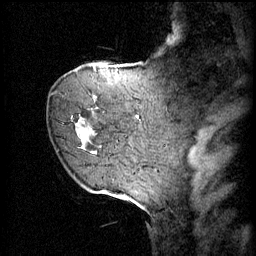
Breast MRI (dynamic contrast-enhanced), one sagittal slice. Position 13 of 60 along the scan axis. 4 images stored at this slice position (order not interpretable as contrast timing). 1.5 T. TE 4.2 ms, TR 11 ms. 2 mm slice thickness. 256 × 256 image matrix. Female patient, age 72 years.
Annotated regions visible in this slice (semi-automatically segmented with operator editing):
- analysis volume of interest (the breast-tissue region the enhancement analysis was run in; not a lesion): bounding box [x1, y1, x2, y2] px = [63, 68, 109, 153]
- tumour enhancement mask (voxels above the 70 % enhancement threshold inside the analysis volume of interest): [79, 68, 108, 145]